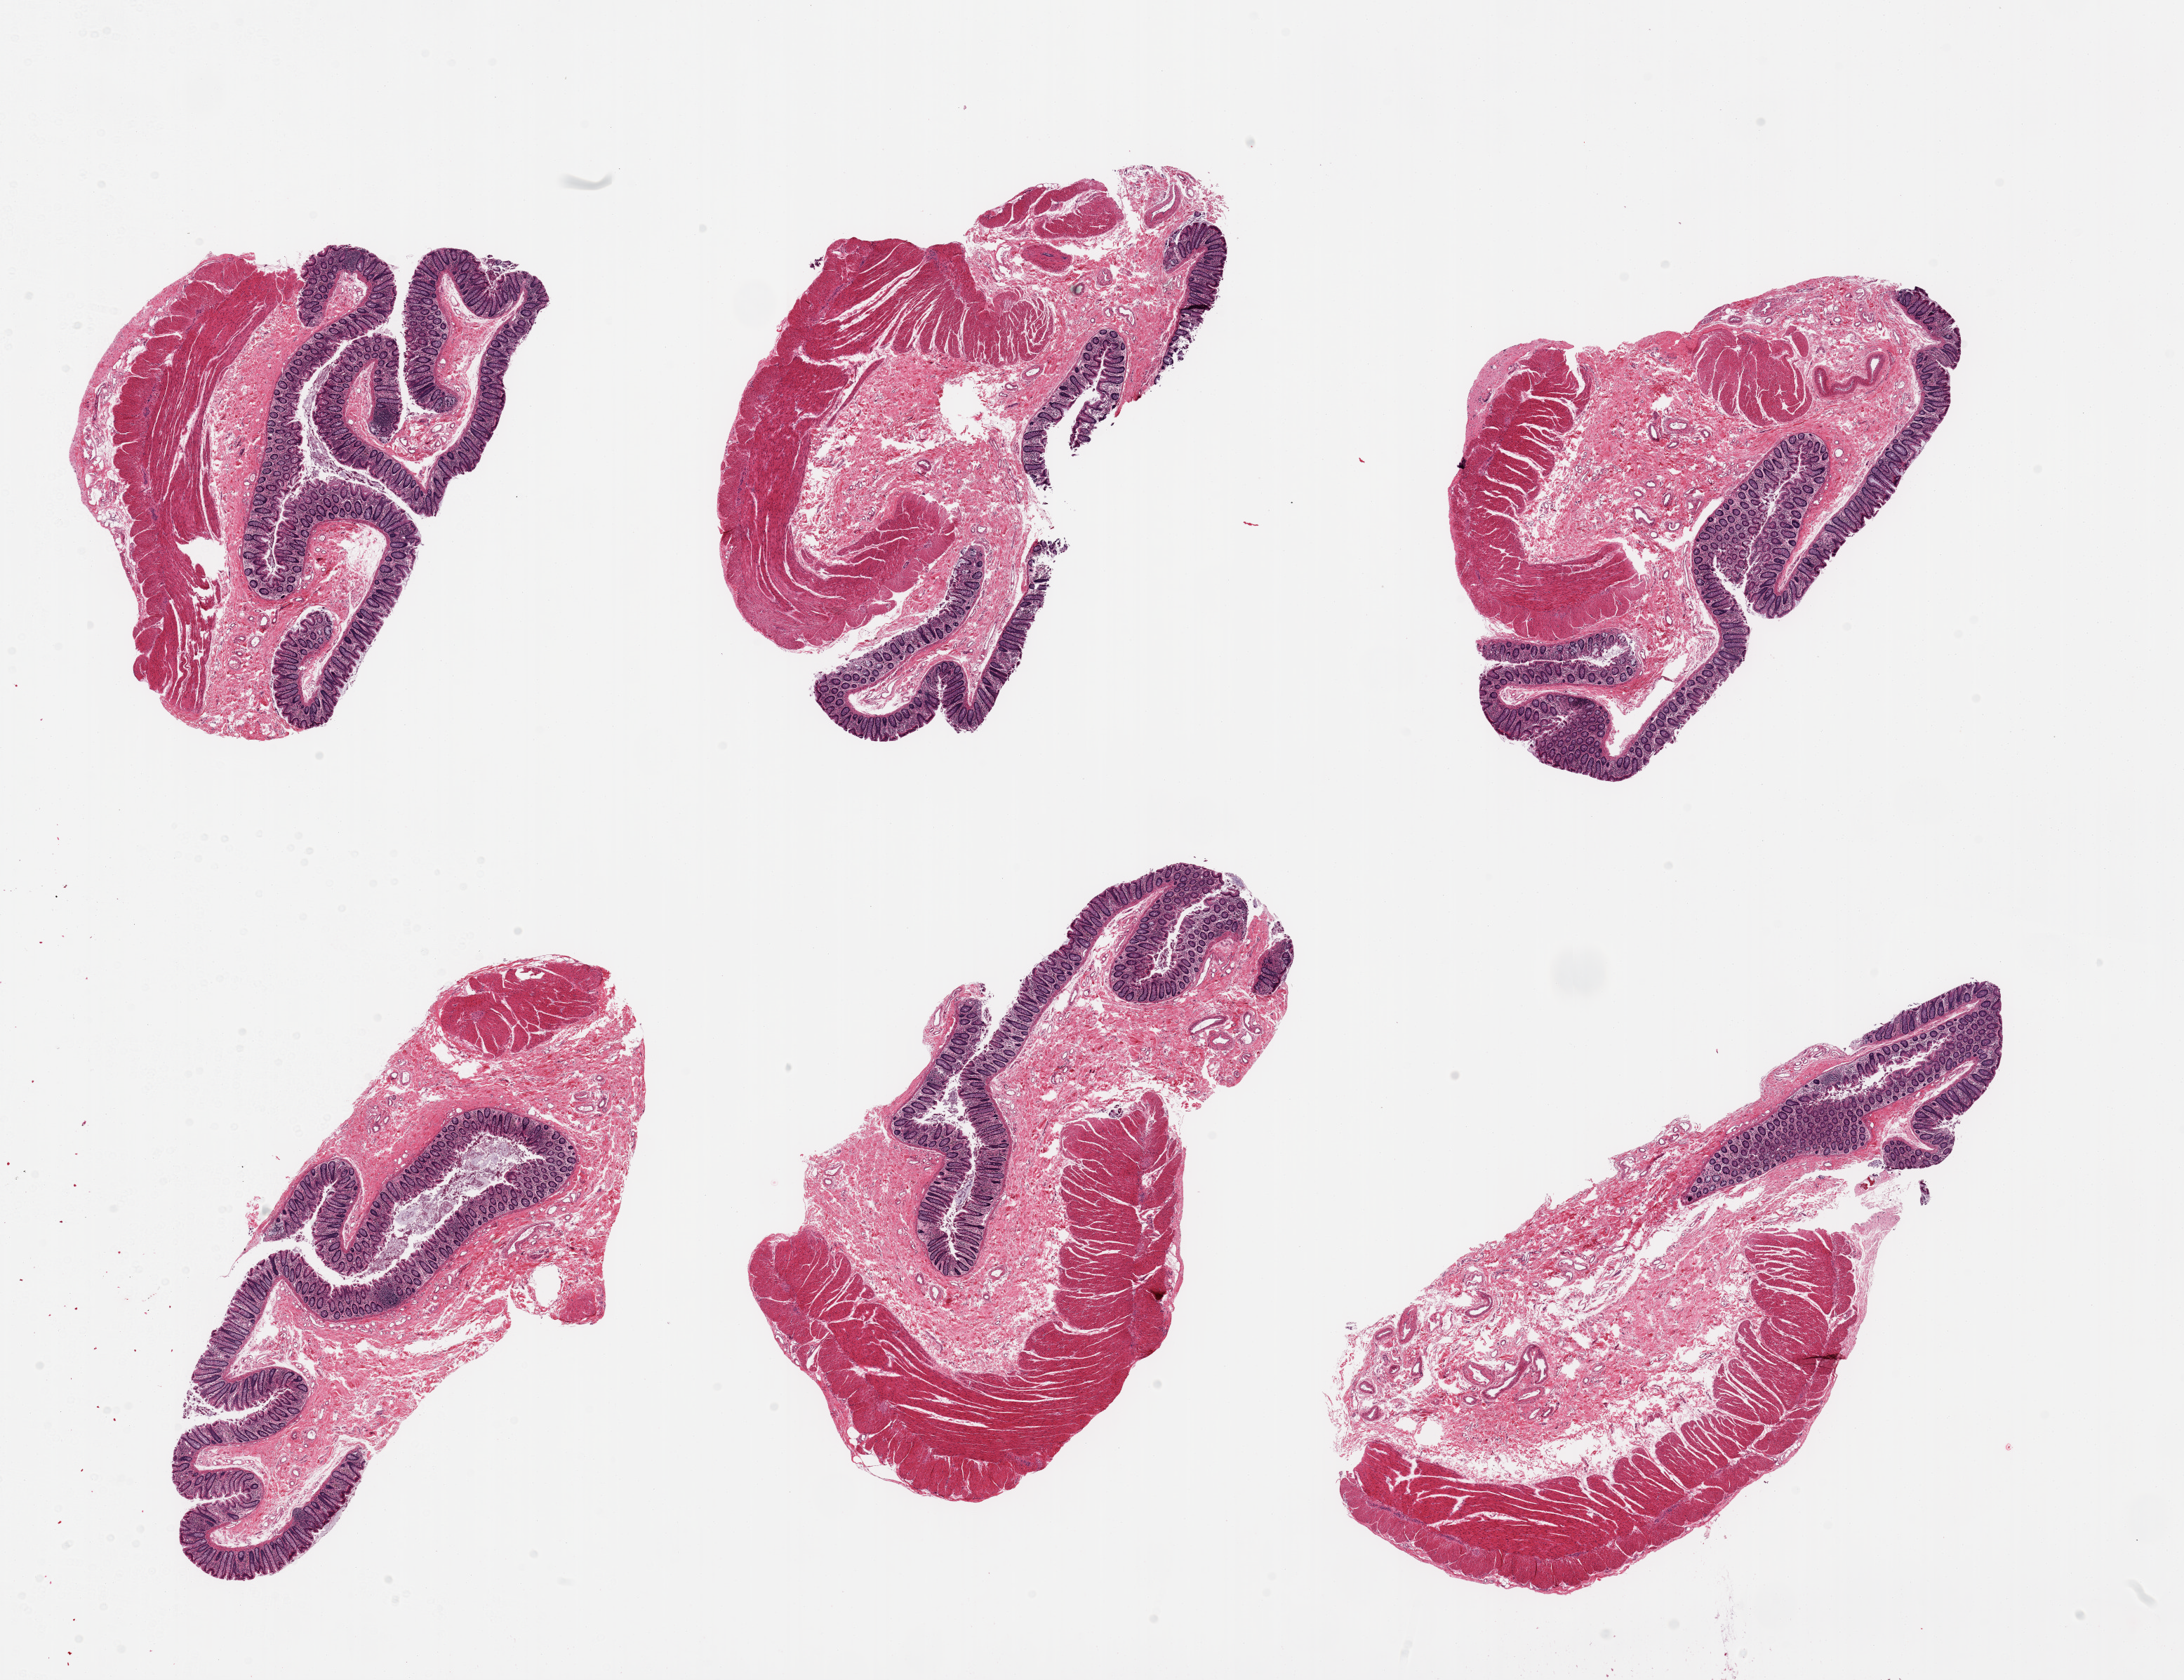
Digitized haematoxylin and eosin-stained section, brightfield, whole scanned area (about 24.6 x 18.9 mm) shown as a low-resolution overview. PAXgene-fixed, paraffin-embedded tissue. Target tissue: transverse colon. Tissue donor sample. Donor: female.
Pathologist's review note for this sample: 6 pieces.